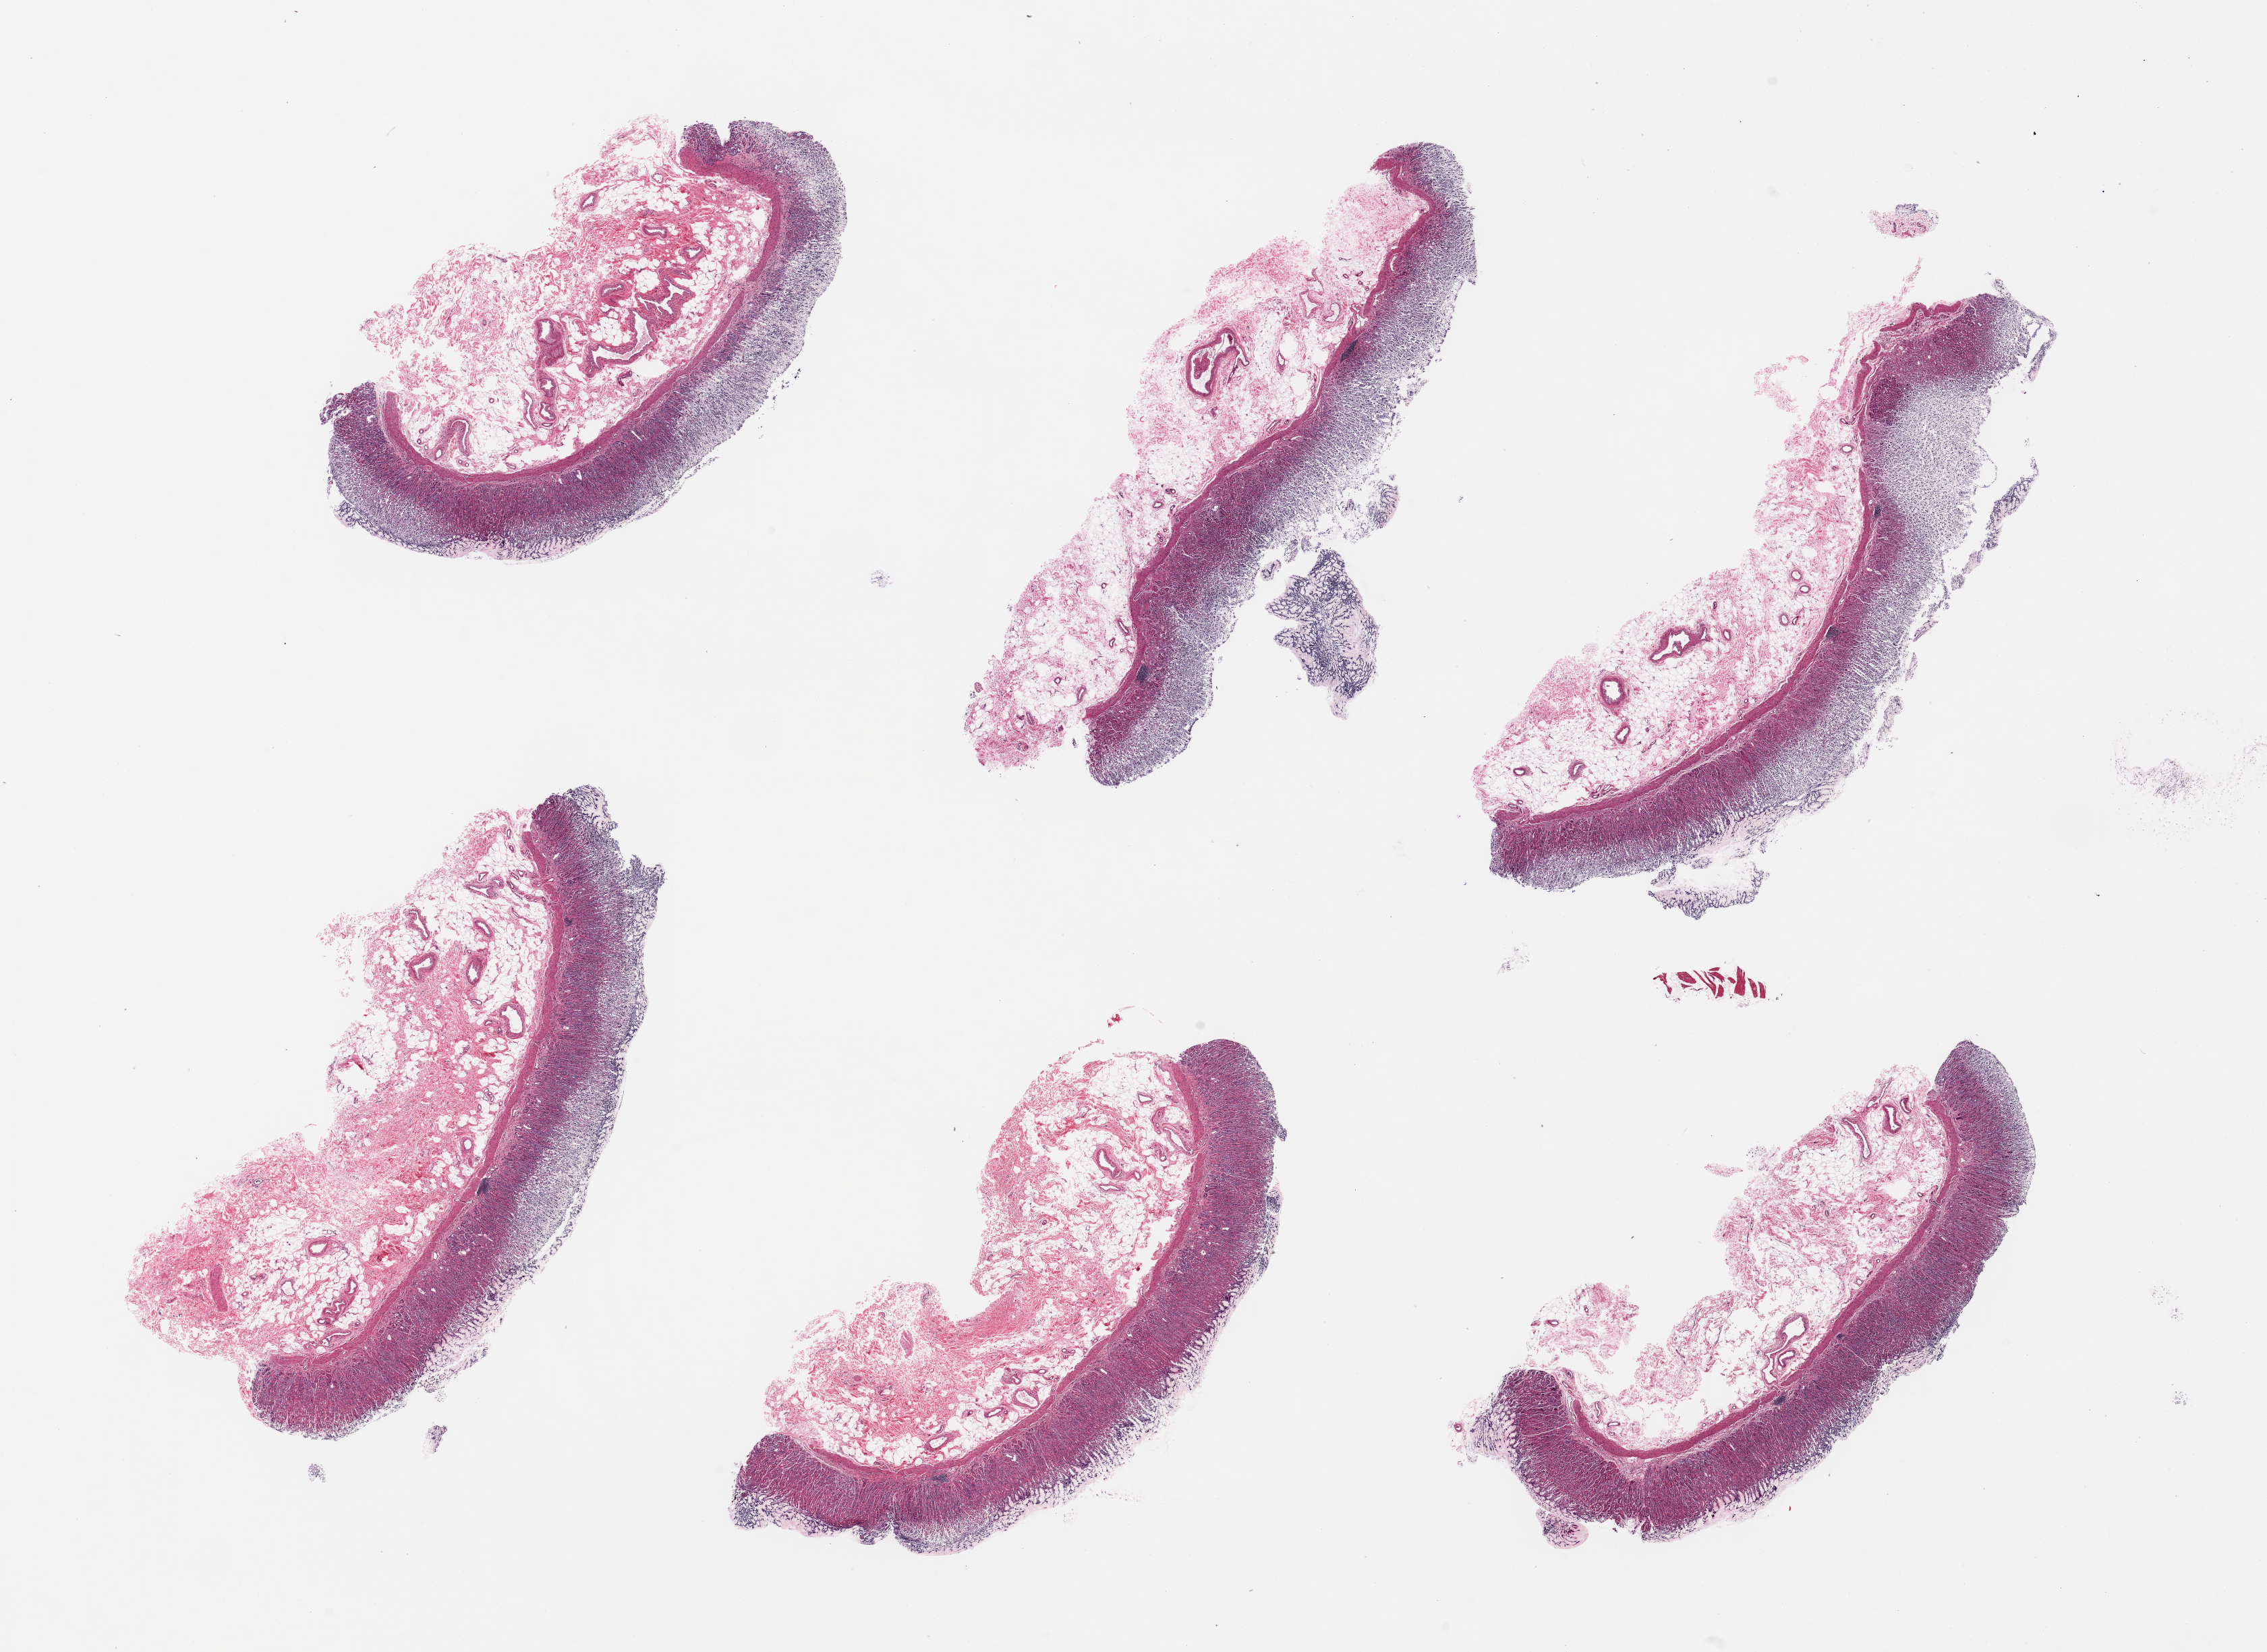
Digitized hematoxylin and eosin (H&E)-stained section, whole scanned area (about 26.6 x 19.4 mm) shown as a low-resolution overview; PAXgene-fixed paraffin-embedded (PFPE) section; sampled site (target tissue): stomach; donor tissue sample. Donor sex: male.
Pathologist's review note for this sample: 6 pieces, superficial part of mucosa is autolyzed.